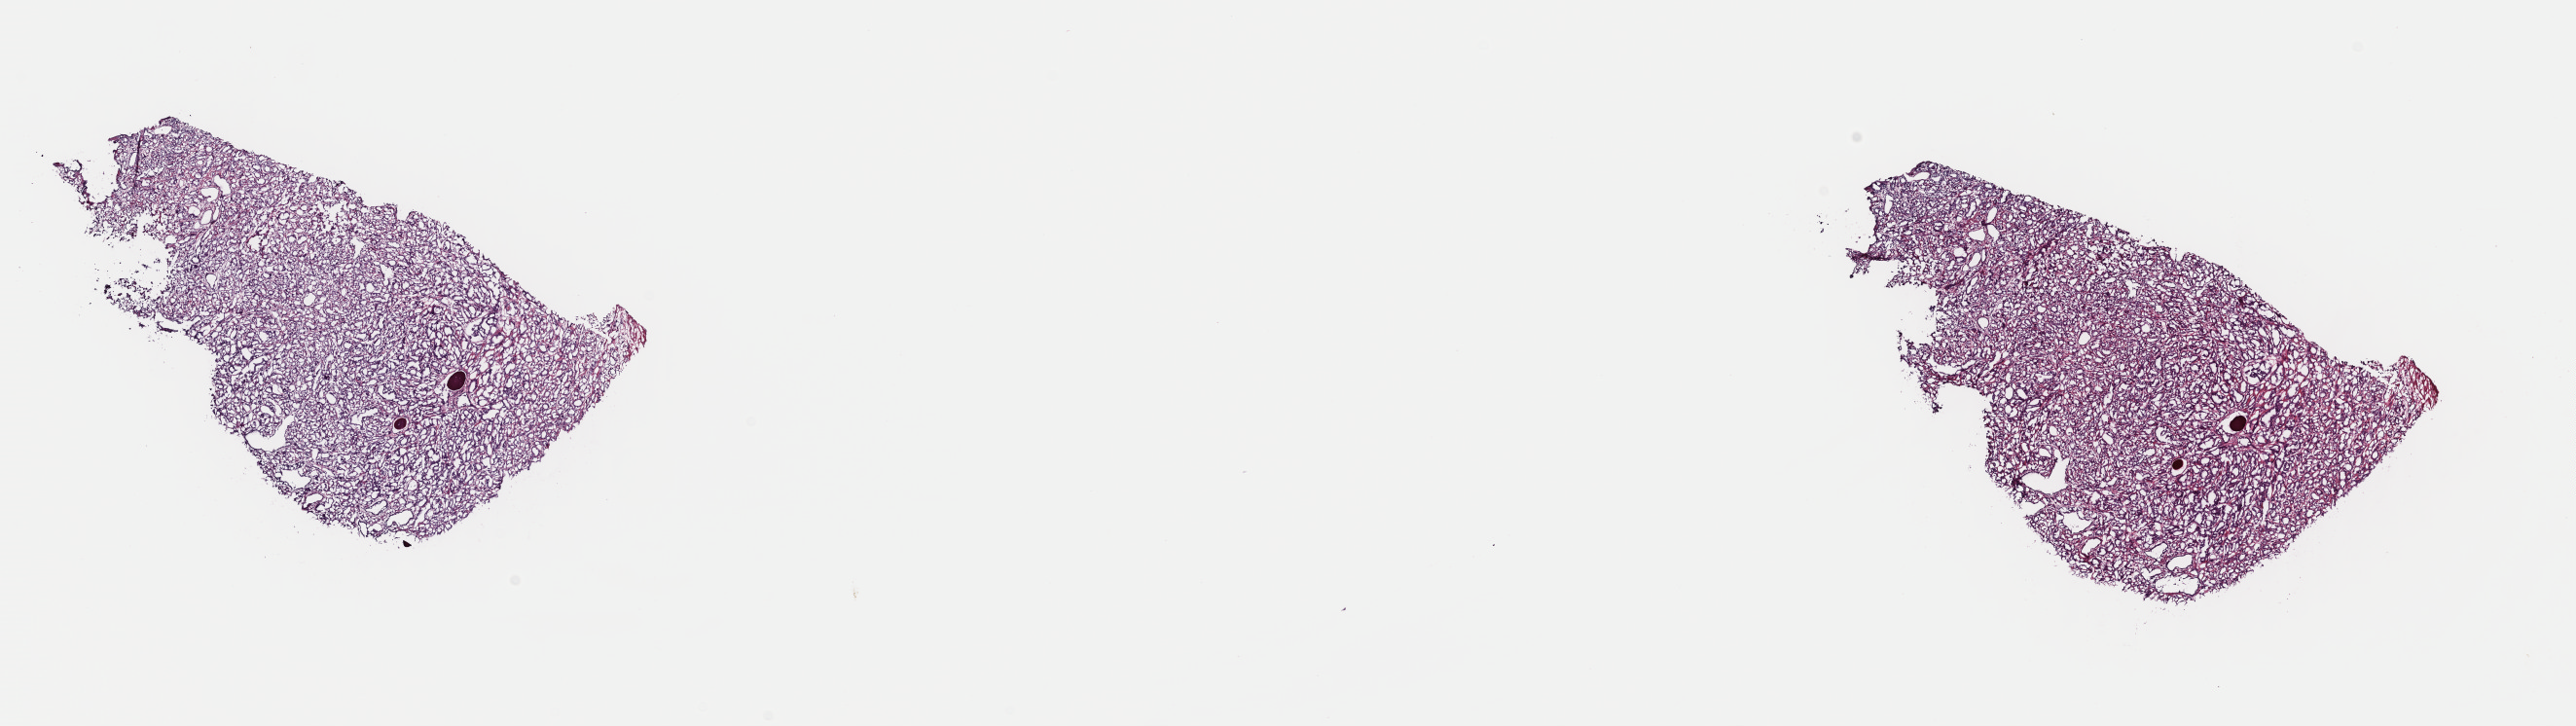
H&E-stained whole-slide image — low-resolution overview of the scanned area, about 20.9 x 5.9 mm (slide scanned at 40x); frozen section from the top of the tissue portion; prostate, primary tumour sample. Patient: male, age at initial diagnosis 59 years. Gleason score: 7 (3+4). Pathologist review of this section (percent, as recorded): tumour cells 70%, tumour nuclei 90%, normal cells 1%, stromal cells 28%, necrosis 1%. Infiltration values recorded for this section: lymphocyte infiltration 2%, monocyte infiltration 0%, neutrophil infiltration 0%.
- histologic diagnosis: Adenocarcinoma, NOS (prostate gland)
- lymph nodes positive (case pathology): 0 of 2 examined